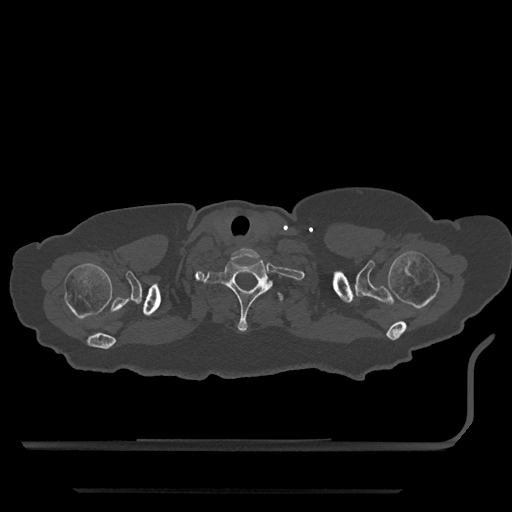
CT including the spine, one axial slice; position 710 of 797 along the scan axis; reconstruction kernel Br40s/3; 120 kVp; bone window (W 1800 / L 400 HU); 0.5 mm slice thickness; 512 × 512 image matrix, field of view 440 × 440 mm. Female patient, age 51 years. Case-level facts recorded for this patient, not image findings: primary cancer: neuro; vertebrae with lytic lesions (as recorded): T8.
Annotated regions visible in this slice (semi-automatically segmented with operator editing):
- T1 vertebra: bounding box [x1, y1, x2, y2] px = [204, 260, 282, 332]
- T2 vertebra: [257, 283, 283, 302]